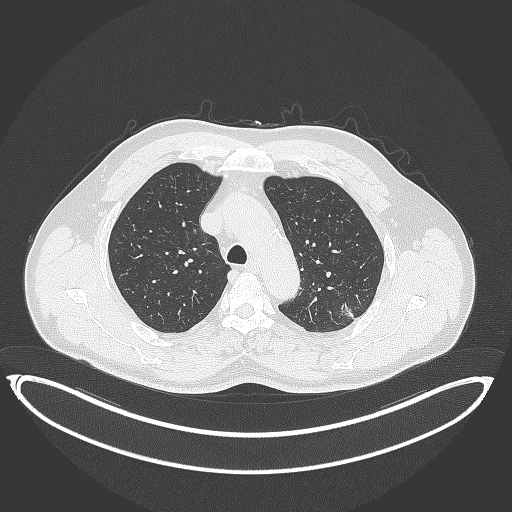
Chest CT, one axial slice; reconstruction kernel B70f; 120 kVp; lung window (W 1500 / L -600 HU); 1 mm slice thickness; 512 × 512 image matrix, field of view 469 × 469 mm. Male patient, age 58 years. Case-level facts recorded for this patient, not image findings: clinical TNM (as recorded): T1c N0 M0; histopathological grade: G1-2.
Structures marked on this image (rectangle marked by the reading radiologist):
- lung tumour (recorded histology: adenocarcinoma): box from (x=337, y=296) to (x=362, y=322) px